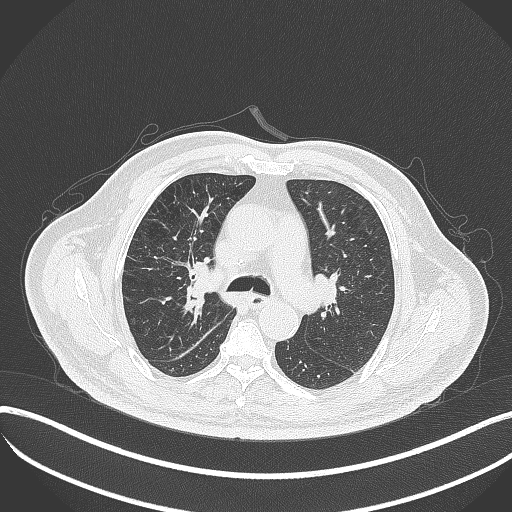
Chest CT, one axial slice. Slice 238 of 401 in the series (ordered by position). Reconstruction kernel B70f. 120 kVp. Lung window (W 1500 / L -600 HU). 1 mm slice thickness. 512 × 512 image matrix, field of view 400 × 400 mm. Patient: male, 72 years. From the clinical record (not read from this slice): clinical TNM (as recorded): T1c N0 M0; histopathological grade: G2.
Outlined on this slice (rectangle marked by the reading radiologist):
- lung tumour (recorded histology: squamous cell carcinoma): bounding box [x1, y1, x2, y2] px = [180, 264, 212, 303]